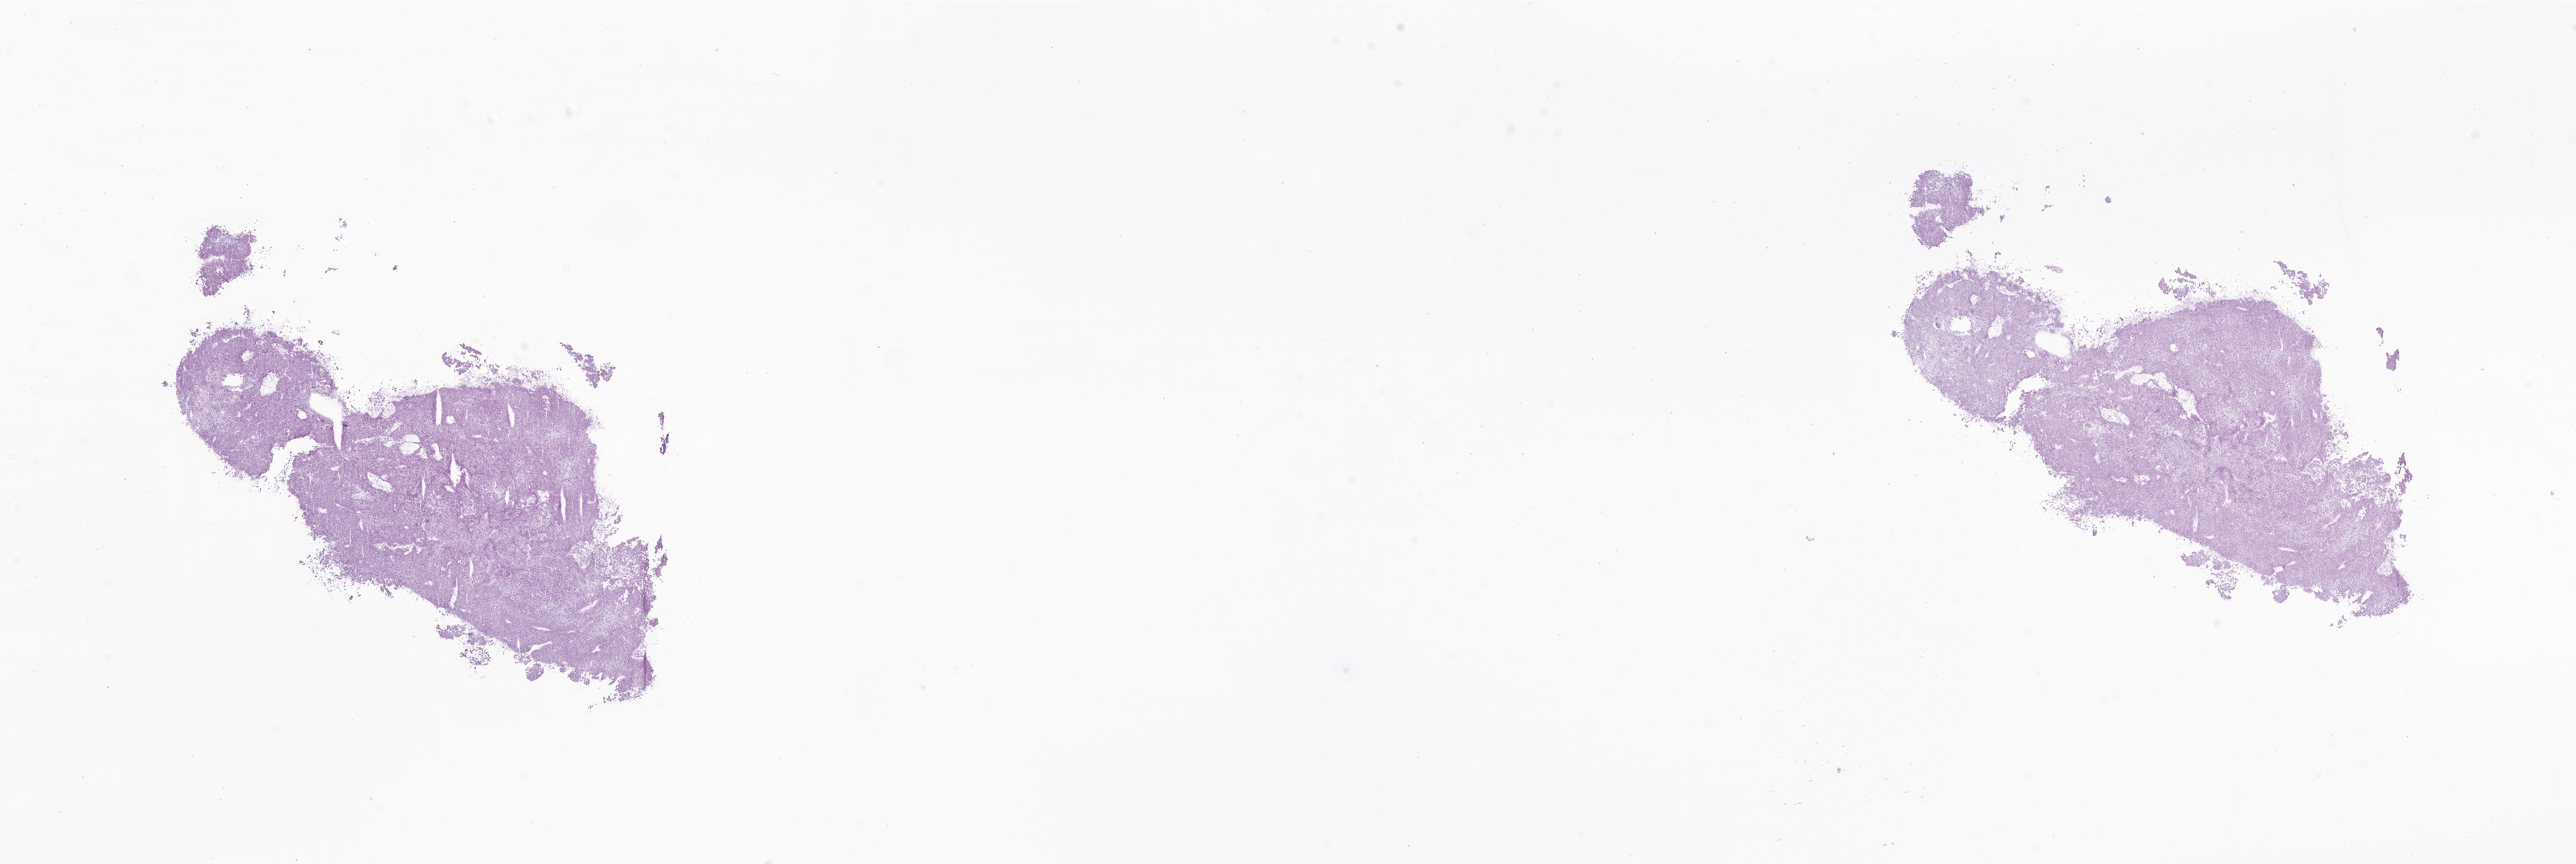
H&E whole-slide image of tumor tissue from the adrenal cortex, a low-resolution overview of the entire scanned area, about 29.5 x 9.9 mm. Cryosection (OCT / tissue freezing medium). Male patient, age 48 months (4 years).
Diagnosis (ICD-O-3 morphology term): Adrenal cortical carcinoma.